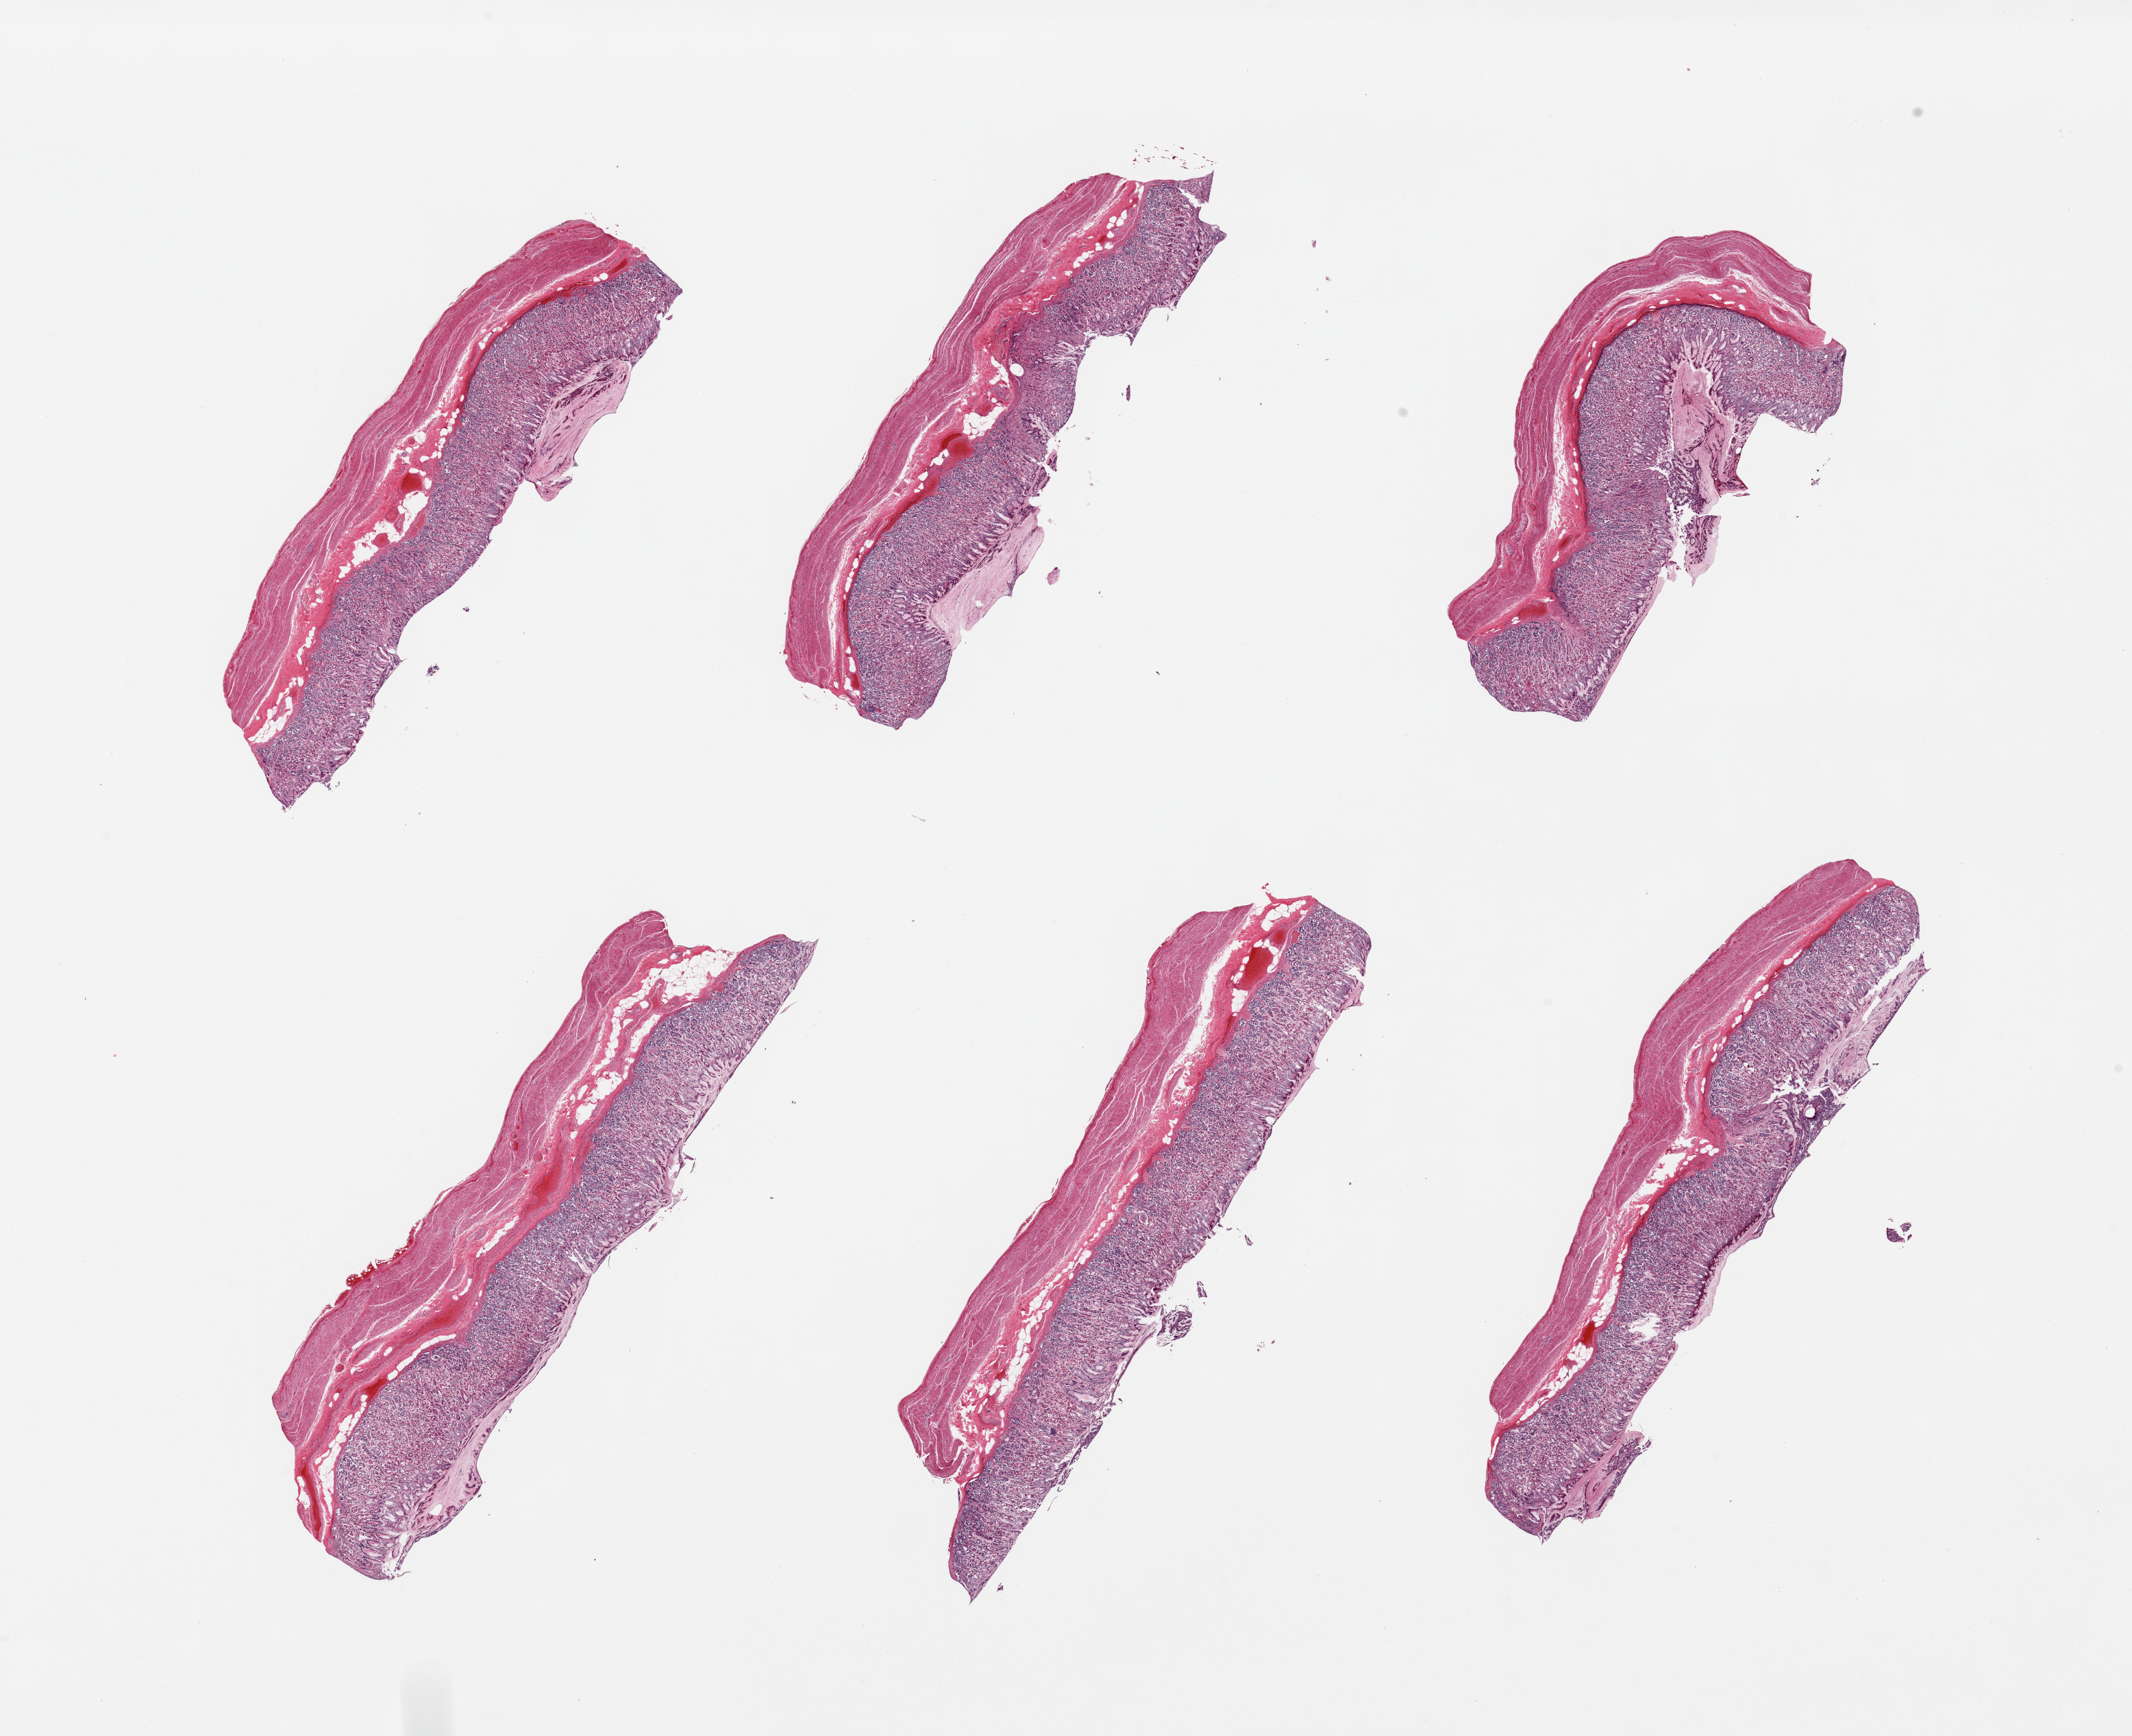
Digitized hematoxylin and eosin (H&E)-stained section — a low-resolution overview of the entire scanned area, about 24.6 x 20.0 mm (slide scanned at 20x). PAXgene-fixed paraffin-embedded (PFPE) section. Section of stomach (target tissue). Tissue donor sample. Donor sex: female.
* reviewer comment on this tissue sample: 6 pieces, mucosa moderately autolyzed, 40-60% thickness